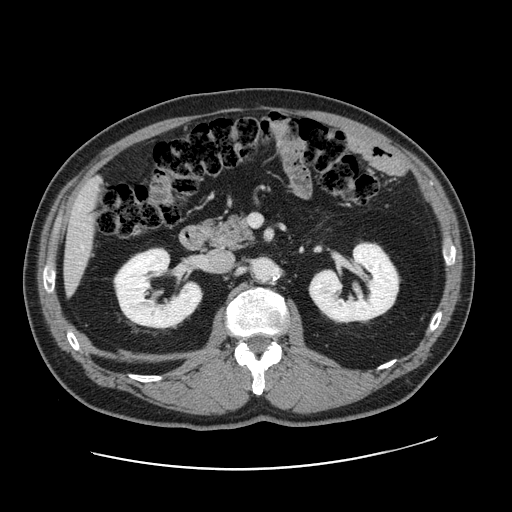
Contrast-enhanced abdominal CT, one axial slice. 120 kVp. Intravenous contrast given. Soft-tissue window (W 400 / L 40 HU). 2.5 mm slice thickness. 512 × 512 image matrix. Male patient, age 63 years. From the clinical record (not read from this slice): diagnosis: colorectal cancer liver metastases, imaged before liver resection; multiple liver metastases: yes; largest metastasis: 8 cm.
Structures marked on this image (manually delineated by an expert):
- liver: bounding box <65,181,100,289> (left, top, right, bottom; pixels)